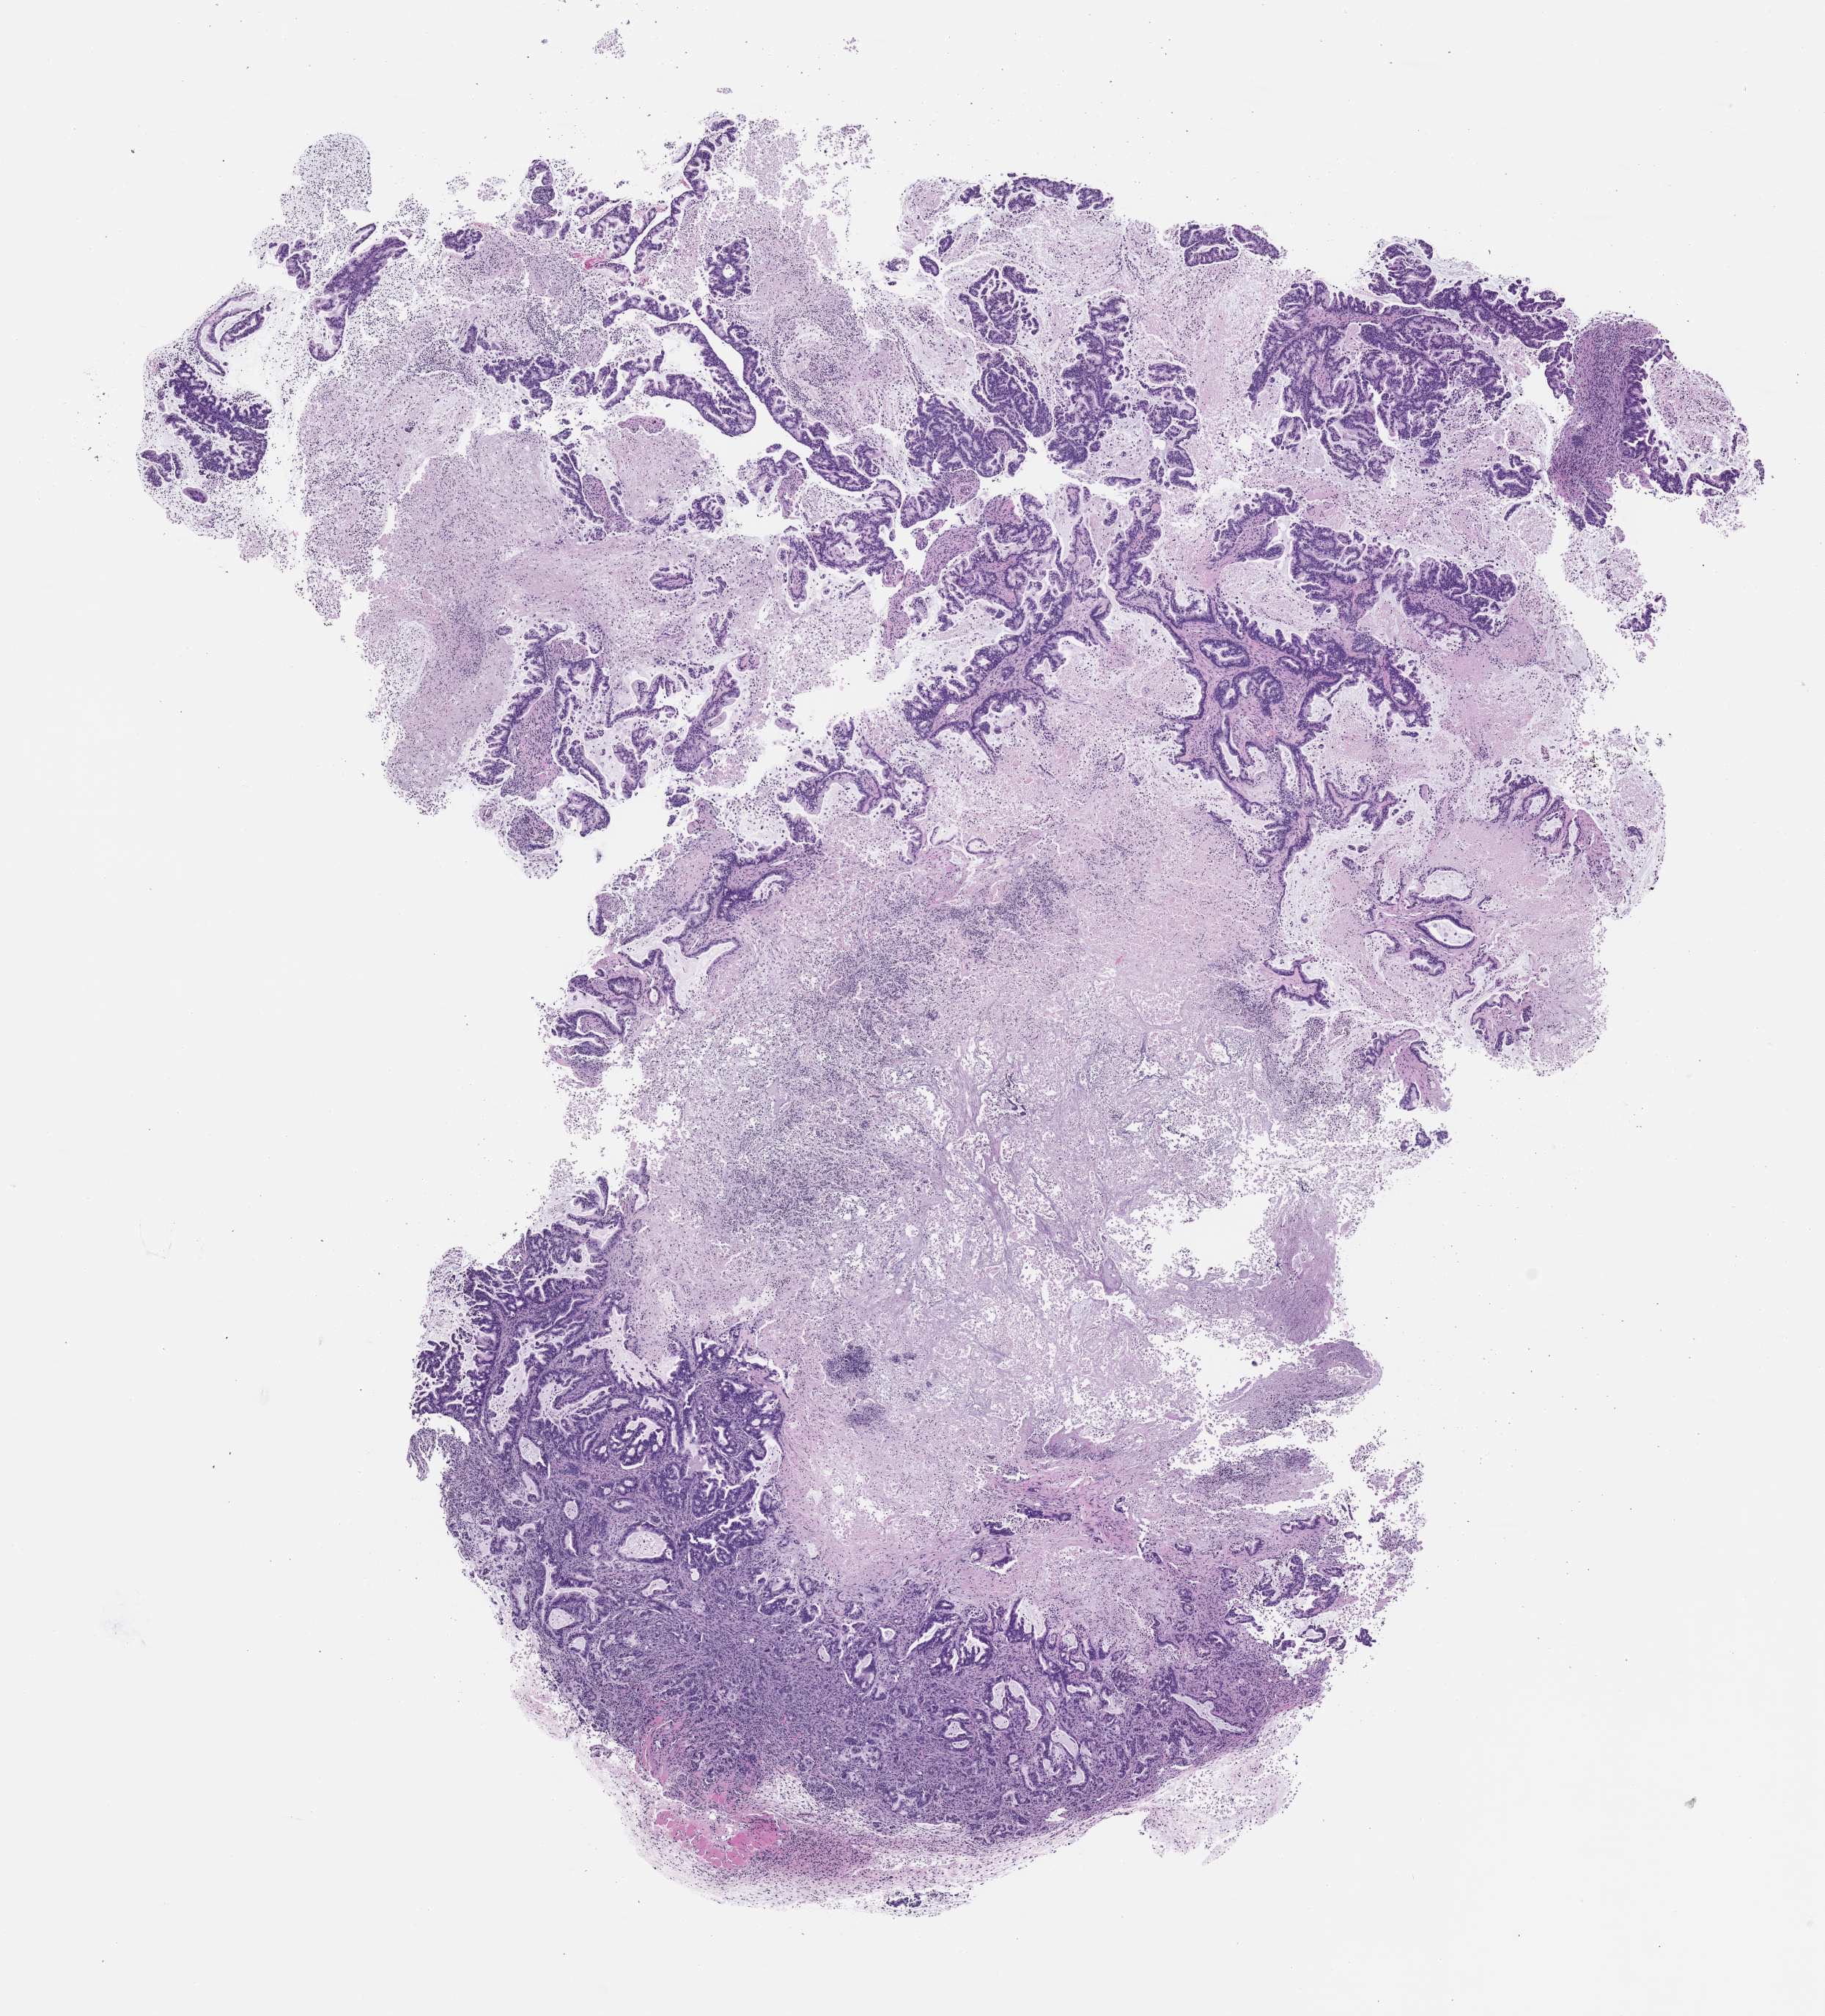
Haematoxylin and eosin whole-slide image of a patient-derived xenograft (PDX) tumor grown in a mouse, passage 1, shown as a low-resolution overview of the whole scanned area (about 10.0 x 11.1 mm); formalin-fixed paraffin-embedded section; tumor site category: pancreas.
- originating patient diagnosis: Pancreatic Adenocarcinoma